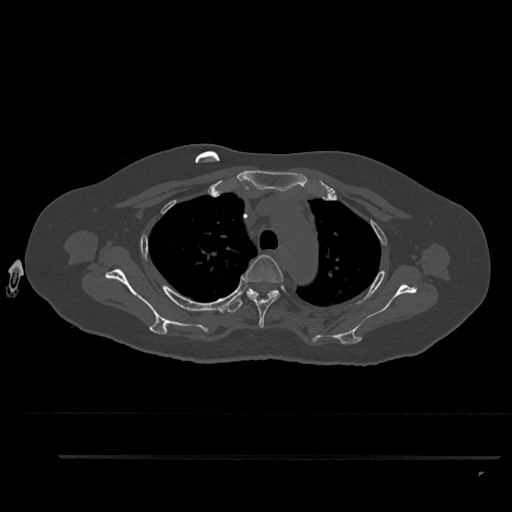
CT including the spine, one axial slice. Slice 668 of 797 in the series (ordered by position). Reconstruction kernel Br40s/3. 120 kVp. Bone window (W 1800 / L 400 HU). 0.5 mm slice thickness. 512 × 512 image matrix, field of view 408 × 408 mm. Female patient, age 44 years. From the clinical record (not read from this slice): primary cancer: renal.
Outlined on this slice (semi-automatically segmented with operator editing):
- T3 vertebra: bounding box <241,255,284,328> (left, top, right, bottom; pixels)
- T4 vertebra: <227,288,279,313>